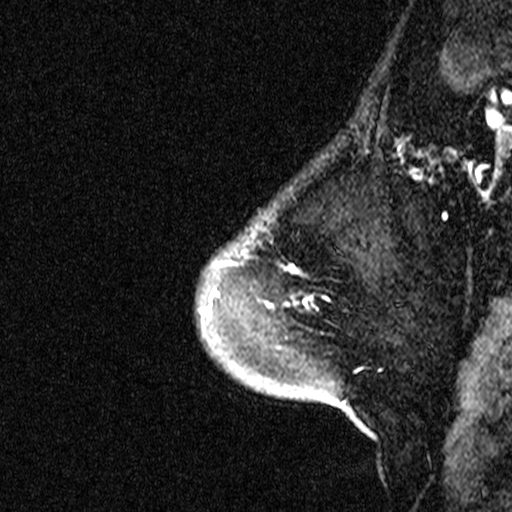
Breast MRI (dynamic contrast-enhanced), one sagittal slice. Slice 7 of 44 in the series (ordered by position). Dynamic contrast-enhanced study with each time point stored as its own series, time point 2 of 3 at this slice position (early post-contrast, ordered by acquisition time). 1.5 T. TE 4.5 ms, TR 11 ms. 3 mm slice thickness. 512 × 512 image matrix, field of view 200 × 200 mm. Patient: female, 46 years. From the clinical record (not read from this slice): setting: breast cancer imaged before/during neoadjuvant chemotherapy; receptor status: HER2-positive.
Outlined on this slice (semi-automatically segmented with operator editing):
- analysis volume of interest (the breast-tissue region the enhancement analysis was run in; not a lesion): bounding box [x1, y1, x2, y2] px = [206, 172, 359, 393]
- tumour enhancement mask (voxels above the 90 % enhancement threshold inside the analysis volume of interest): [264, 270, 297, 347]